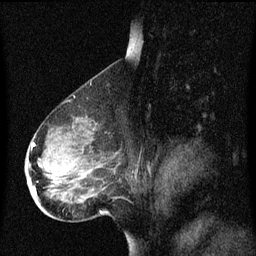
Breast MRI (dynamic contrast-enhanced), one sagittal slice. Slice 43 of 60 in the series (ordered by position). Dynamic contrast-enhanced series, image 2 of 3 at this slice position (ordered by acquisition). 1.5 T. TE 4.2 ms, TR 8.4 ms. 2 mm slice thickness. 256 × 256 image matrix. Female patient, age 49 years. Case-level facts recorded for this patient, not image findings: setting: breast cancer imaged before/during neoadjuvant chemotherapy; receptor status: HR-positive, HER2-negative.
Annotated regions visible in this slice (semi-automatic segmentation, software-assisted and operator-edited):
- analysis volume of interest (the breast-tissue region the enhancement analysis was run in; not a lesion): bounding box <26,126,101,201> (left, top, right, bottom; pixels)
- tumour enhancement mask (voxels above the 70 % enhancement threshold inside the analysis volume of interest): <33,142,37,195>